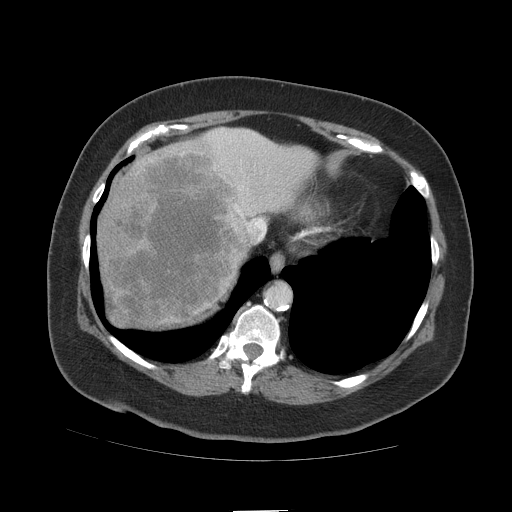
Contrast-enhanced abdominal CT (liver protocol), one axial slice. Slice 90 of 109 in the series (ordered by position). Reconstruction kernel STANDARD. 140 kVp. Soft-tissue window (W 400 / L 40 HU). 512 × 512 image matrix. Case-level facts recorded for this patient, not image findings: diagnosis: hepatocellular carcinoma (patient treated with transarterial chemoembolisation; whether this scan precedes or follows treatment is not stated here); TNM stage (as recorded): Stage-IVB; Child-Pugh class: A; tumour differentiation: poorly differentiated.
Structures marked on this image (semi-automatically segmented with operator editing):
- liver parenchyma outside the tumour (the mass and vessels are separate outlines, so this box may not span the whole liver): bounding box <96,128,316,326> (left, top, right, bottom; pixels)
- mass: <97,141,249,325>
- liver vessels: <213,129,266,240>